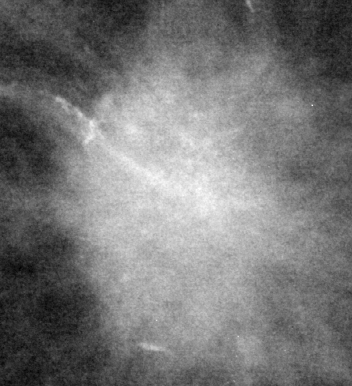
Cropped region of a digitized screen-film mammogram centred on a radiologist-marked abnormality, right breast, CC view, BI-RADS breast density category 2 (scale 1–4).
- Mass, shape irregular / architectural distortion, margins spiculated; BI-RADS assessment category 5; pathology (as recorded): malignant.